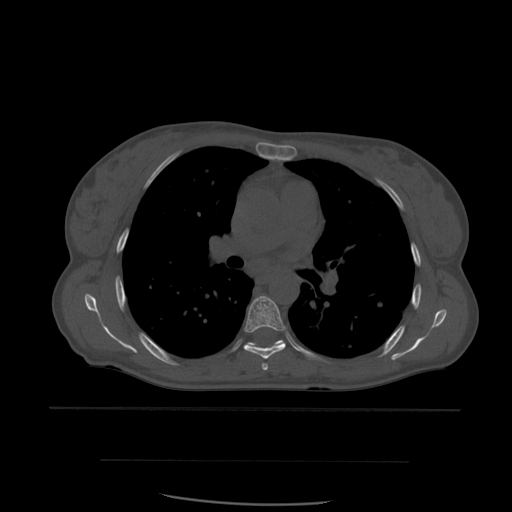
CT including the spine, one axial slice; slice 390 of 574 in the series (ordered by position); bone window (W 1800 / L 400 HU); 1.25 mm slice thickness; 512 × 512 image matrix, field of view 392 × 392 mm. Patient age 48 years. Case-level facts recorded for this patient, not image findings: primary cancer: lung; vertebrae with lytic lesions (as recorded): T11.
Structures marked on this image (semi-automatically segmented with operator editing):
- T5 vertebra: bounding box (x1, y1, x2, y2) in pixels: (262, 363, 269, 371)
- T6 vertebra: (244, 296, 286, 360)
- T7 vertebra: (245, 340, 286, 346)